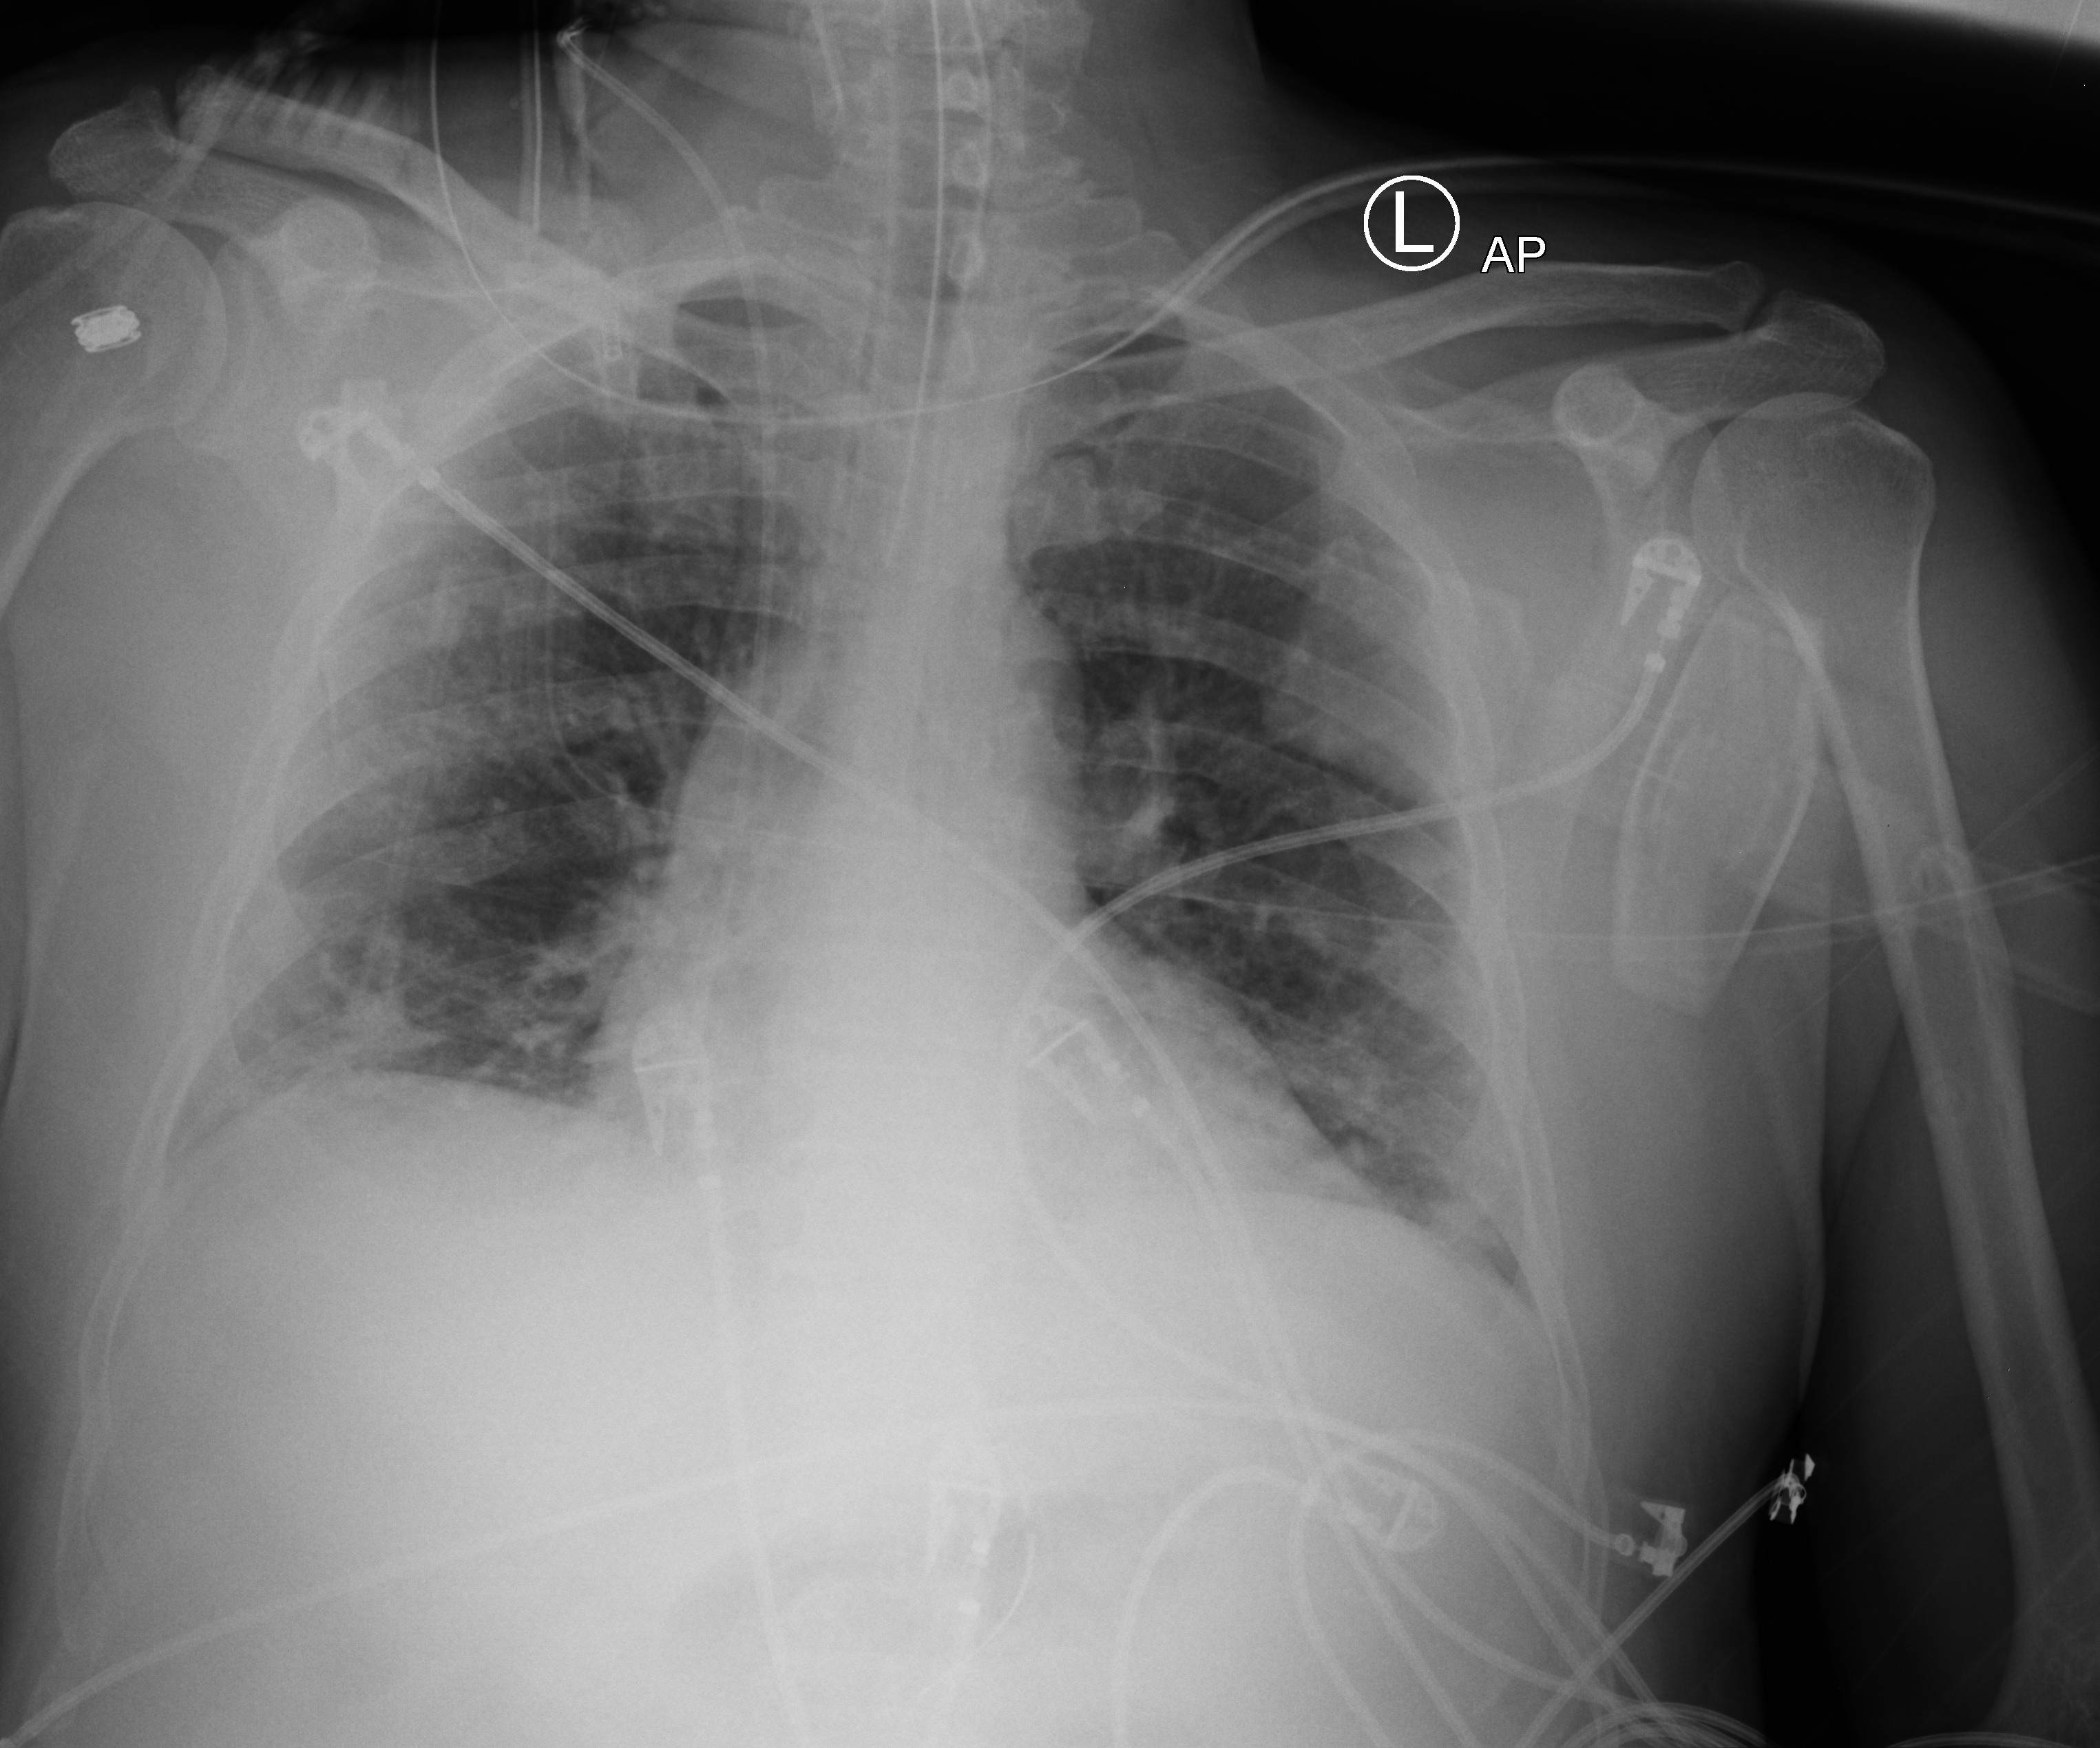
Portable chest radiograph. Patient hospitalised with COVID-19; male, aged 18–59 years.
Hospital-stay facts (about this admission, not read from this image; timing relative to this image not recorded):
- mechanically ventilated during this hospital stay: yes
- hypertension (admission record): no
- COPD (admission record): no